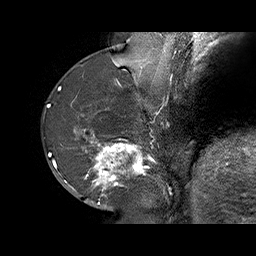
Breast MRI (dynamic contrast-enhanced), one sagittal slice; position 23 of 70 along the scan axis; dynamic contrast-enhanced series, time point 2 of 6 at this slice position (early post-contrast); 1.5 T; TE 4.5 ms, TR 32.4 ms; 256 × 256 image matrix, field of view 180 × 180 mm. Female patient. Case-level facts recorded for this patient, not image findings: setting: breast cancer imaged before/during neoadjuvant chemotherapy; receptor status: HR-positive, HER2-negative.
Structures marked on this image (semi-automatically segmented with operator editing):
- analysis volume of interest (the breast-tissue region the enhancement analysis was run in; not a lesion): box from (x=71, y=128) to (x=159, y=202) px
- tumour enhancement mask (voxels above the 100 % enhancement threshold inside the analysis volume of interest): (x=74, y=129)–(x=149, y=196)